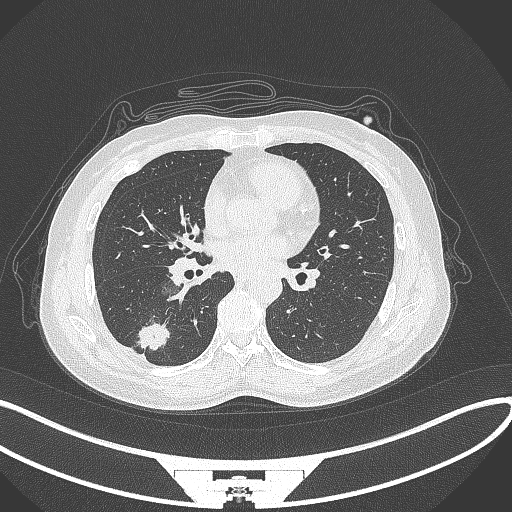
Chest CT, one axial slice; position 141 of 352 along the scan axis; reconstruction kernel B70f; lung window (W 1500 / L -600 HU); 1 mm slice thickness; 512 × 512 image matrix, field of view 400 × 400 mm. Patient: female, 55 years. Case-level facts recorded for this patient, not image findings: clinical TNM (as recorded): T1c N1 M0.
Annotated regions visible in this slice (rectangle marked by the reading radiologist):
- lung tumour (recorded histology: adenocarcinoma): bounding box (x1, y1, x2, y2) in pixels: (135, 318, 173, 355)